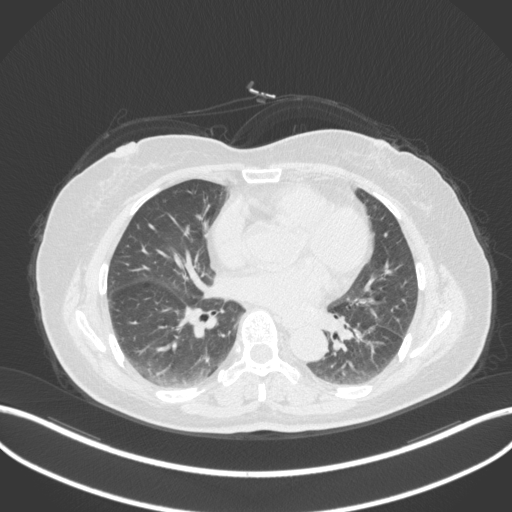
Chest CT, one axial slice; position 171 of 307 along the scan axis; reconstruction kernel B31f; 120 kVp; lung window (W 1500 / L -600 HU); 1 mm slice thickness; 512 × 512 image matrix. Patient: female, 59 years. Case-level facts recorded for this patient, not image findings: clinical TNM (as recorded): T2a N0 M0; histopathological grade: G2-3.
Outlined on this slice (rectangle marked by the reading radiologist):
- lung tumour (recorded histology: adenocarcinoma): bounding box [x1, y1, x2, y2] px = [351, 325, 387, 370]